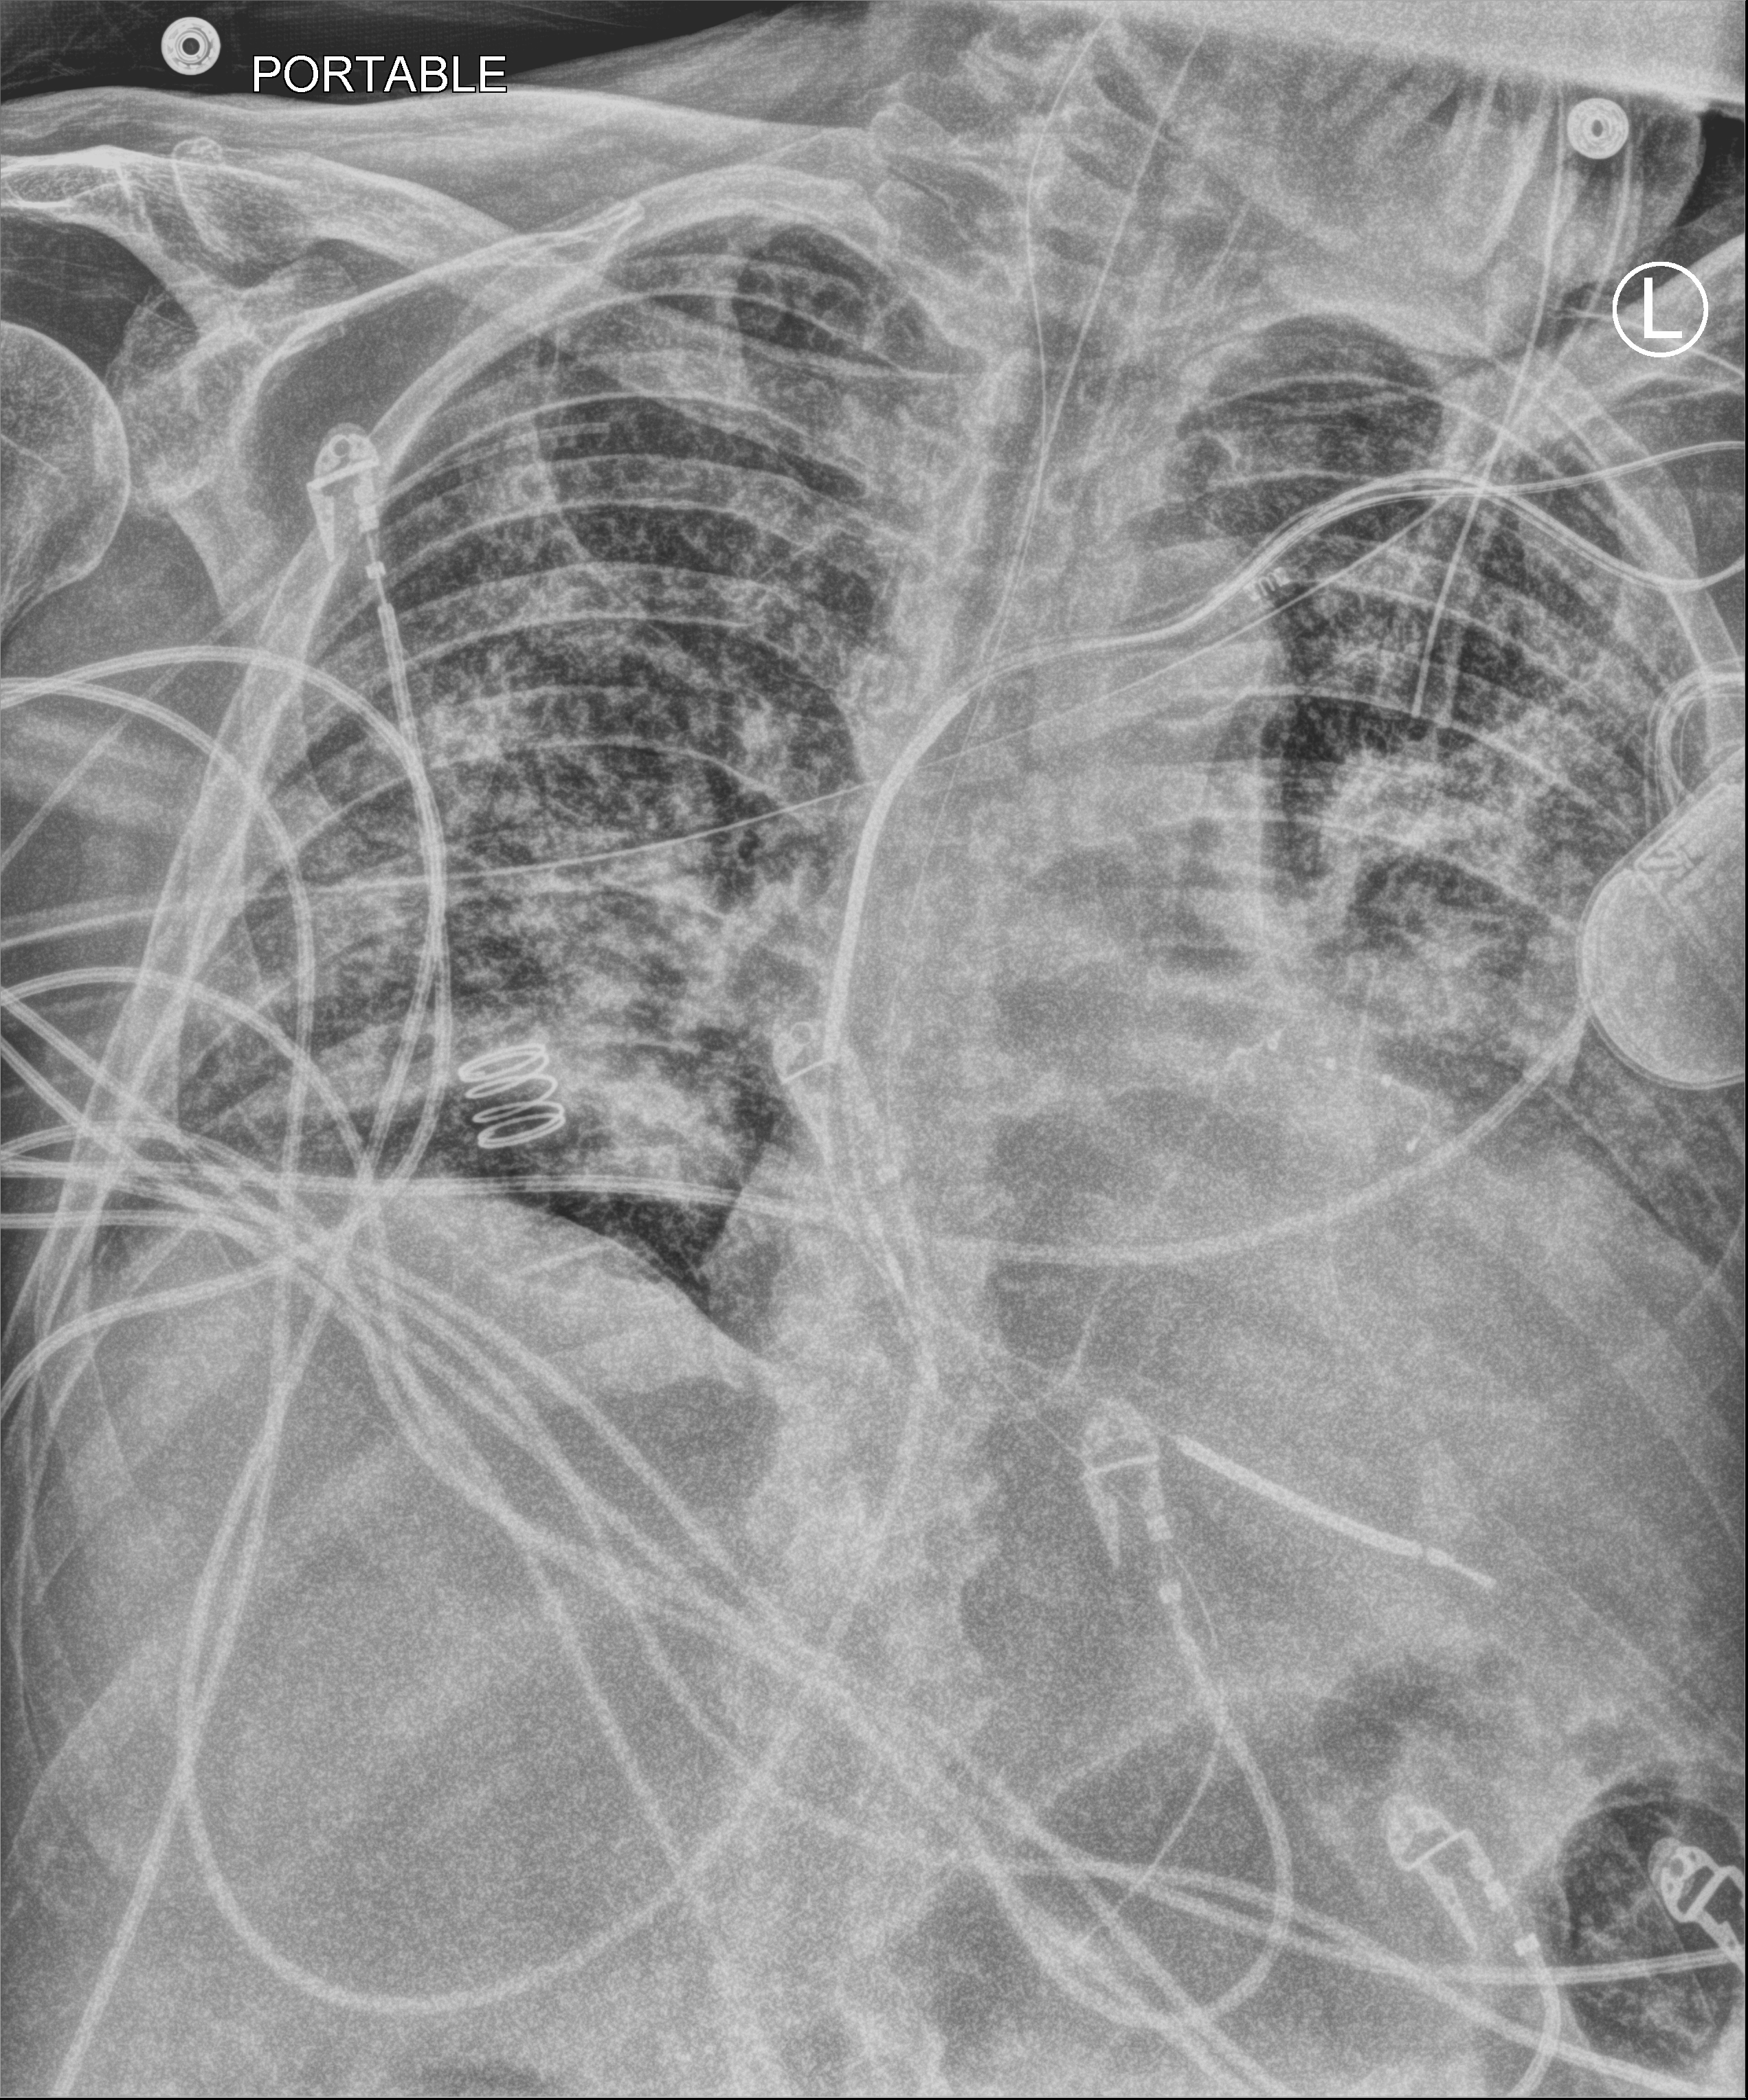
Bedside chest radiograph (computed radiography); anteroposterior (AP) projection. Male patient hospitalised with COVID-19, age 60–74 years.
Admission-level facts for this patient (not findings on this image; timing relative to this image not recorded): admitted to intensive care during this hospital stay: yes; mechanically ventilated during this hospital stay: yes.